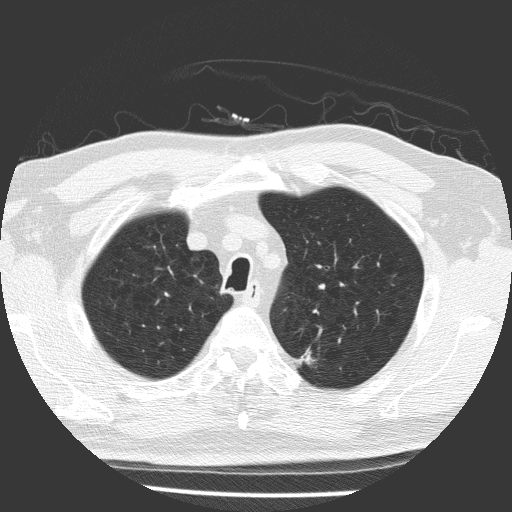
Low-dose screening chest CT, one axial slice; position 136 of 169 along the scan axis; 120 kVp; lung window (W 1500 / L -600 HU); 2 mm slice thickness; 512 × 512 image matrix, field of view 323 × 323 mm.
Structures marked on this image (manually delineated by an expert):
- lesion 1 (tumor, upper lobe of left lung): box from (x=296, y=350) to (x=316, y=367) px